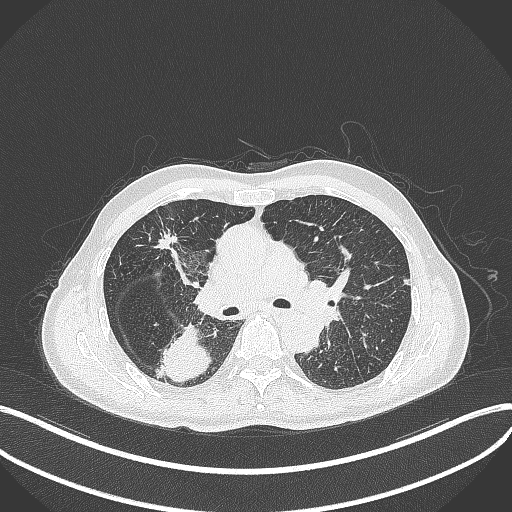
Chest CT, one axial slice. Position 274 of 428 along the scan axis. Reconstruction kernel B70f. Lung window (W 1500 / L -600 HU). 512 × 512 image matrix, field of view 400 × 400 mm. Patient: male, 79 years. From the clinical record (not read from this slice): clinical TNM (as recorded): T3 N0 M0.
Outlined on this slice (rectangle marked by the reading radiologist):
- lung tumour (recorded histology: adenocarcinoma): box from (x=163, y=319) to (x=215, y=384) px